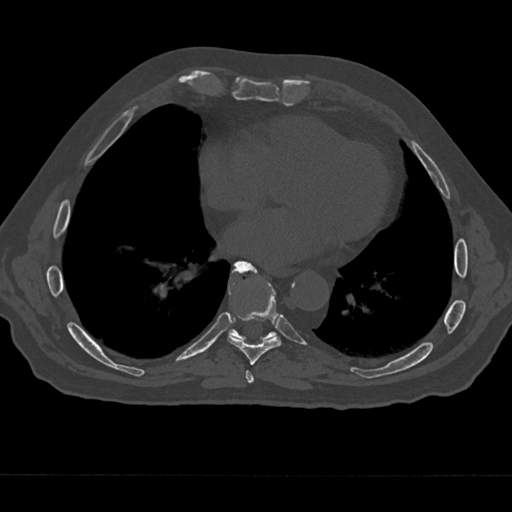
CT including the spine, one axial slice. Position 300 of 797 along the scan axis. Bone window (W 1800 / L 400 HU). 0.5 mm slice thickness. 512 × 512 image matrix. Patient: male, 75 years. From the clinical record (not read from this slice): primary cancer: renal.
Outlined on this slice (semi-automatic segmentation, software-assisted and operator-edited):
- T7 vertebra: box from (x=241, y=368) to (x=255, y=385) px
- T8 vertebra: (x=227, y=265)–(x=282, y=365)
- T9 vertebra: (x=228, y=261)–(x=277, y=341)